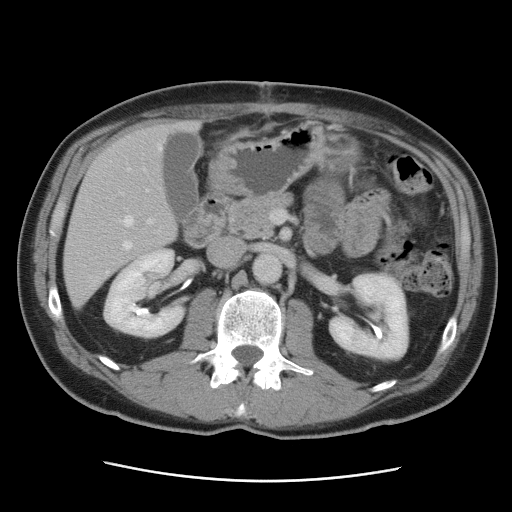
Contrast-enhanced abdominal CT, one axial slice; position 41 of 89 along the scan axis; soft-tissue window (W 400 / L 40 HU); 512 × 512 image matrix, field of view 366 × 366 mm. Male patient, age 59 years. Case-level facts recorded for this patient, not image findings: diagnosis: colorectal cancer liver metastases, imaged before liver resection; multiple liver metastases: yes; largest metastasis: 0.6 cm; disease in both lobes: yes.
Annotated regions visible in this slice (expert manual segmentation):
- hepatic veins: bounding box (x1, y1, x2, y2) in pixels: (94, 145, 162, 284)
- liver: (65, 120, 199, 308)
- planned liver remnant (the part of the liver to remain after resection): (73, 121, 200, 245)
- portal vein (with intrahepatic branches): (121, 189, 153, 224)